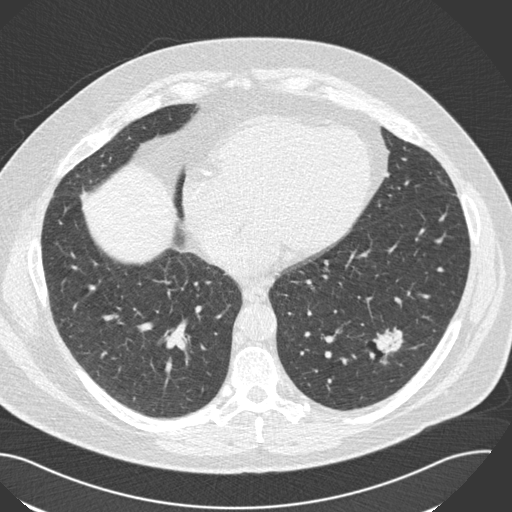
Low-dose screening chest CT, axial slice. Third screening round (two years after baseline). Lung window (W 1500 / L -600 HU). 2 mm slice thickness. Male, age 57 years at enrolment.
Expert reader's lesion annotation, bounding box (x1, y1, x2, y2) in pixels: (349, 317, 421, 376). Reader record for this screening exam (exam-level; its link to the box is not recorded): non-calcified nodule or mass ≥4 mm, left lower lobe, 22 × 18 mm, poorly defined margins, soft tissue attenuation, pre-existing on the prior screen: yes; interval growth: yes. Official screen result: positive, other. Lung cancer was diagnosed 124 days after this screen: squamous cell carcinoma, NOS, left lower lobe, moderately differentiated (G2), stage IA (AJCC 6th edition), 22 mm at pathology.